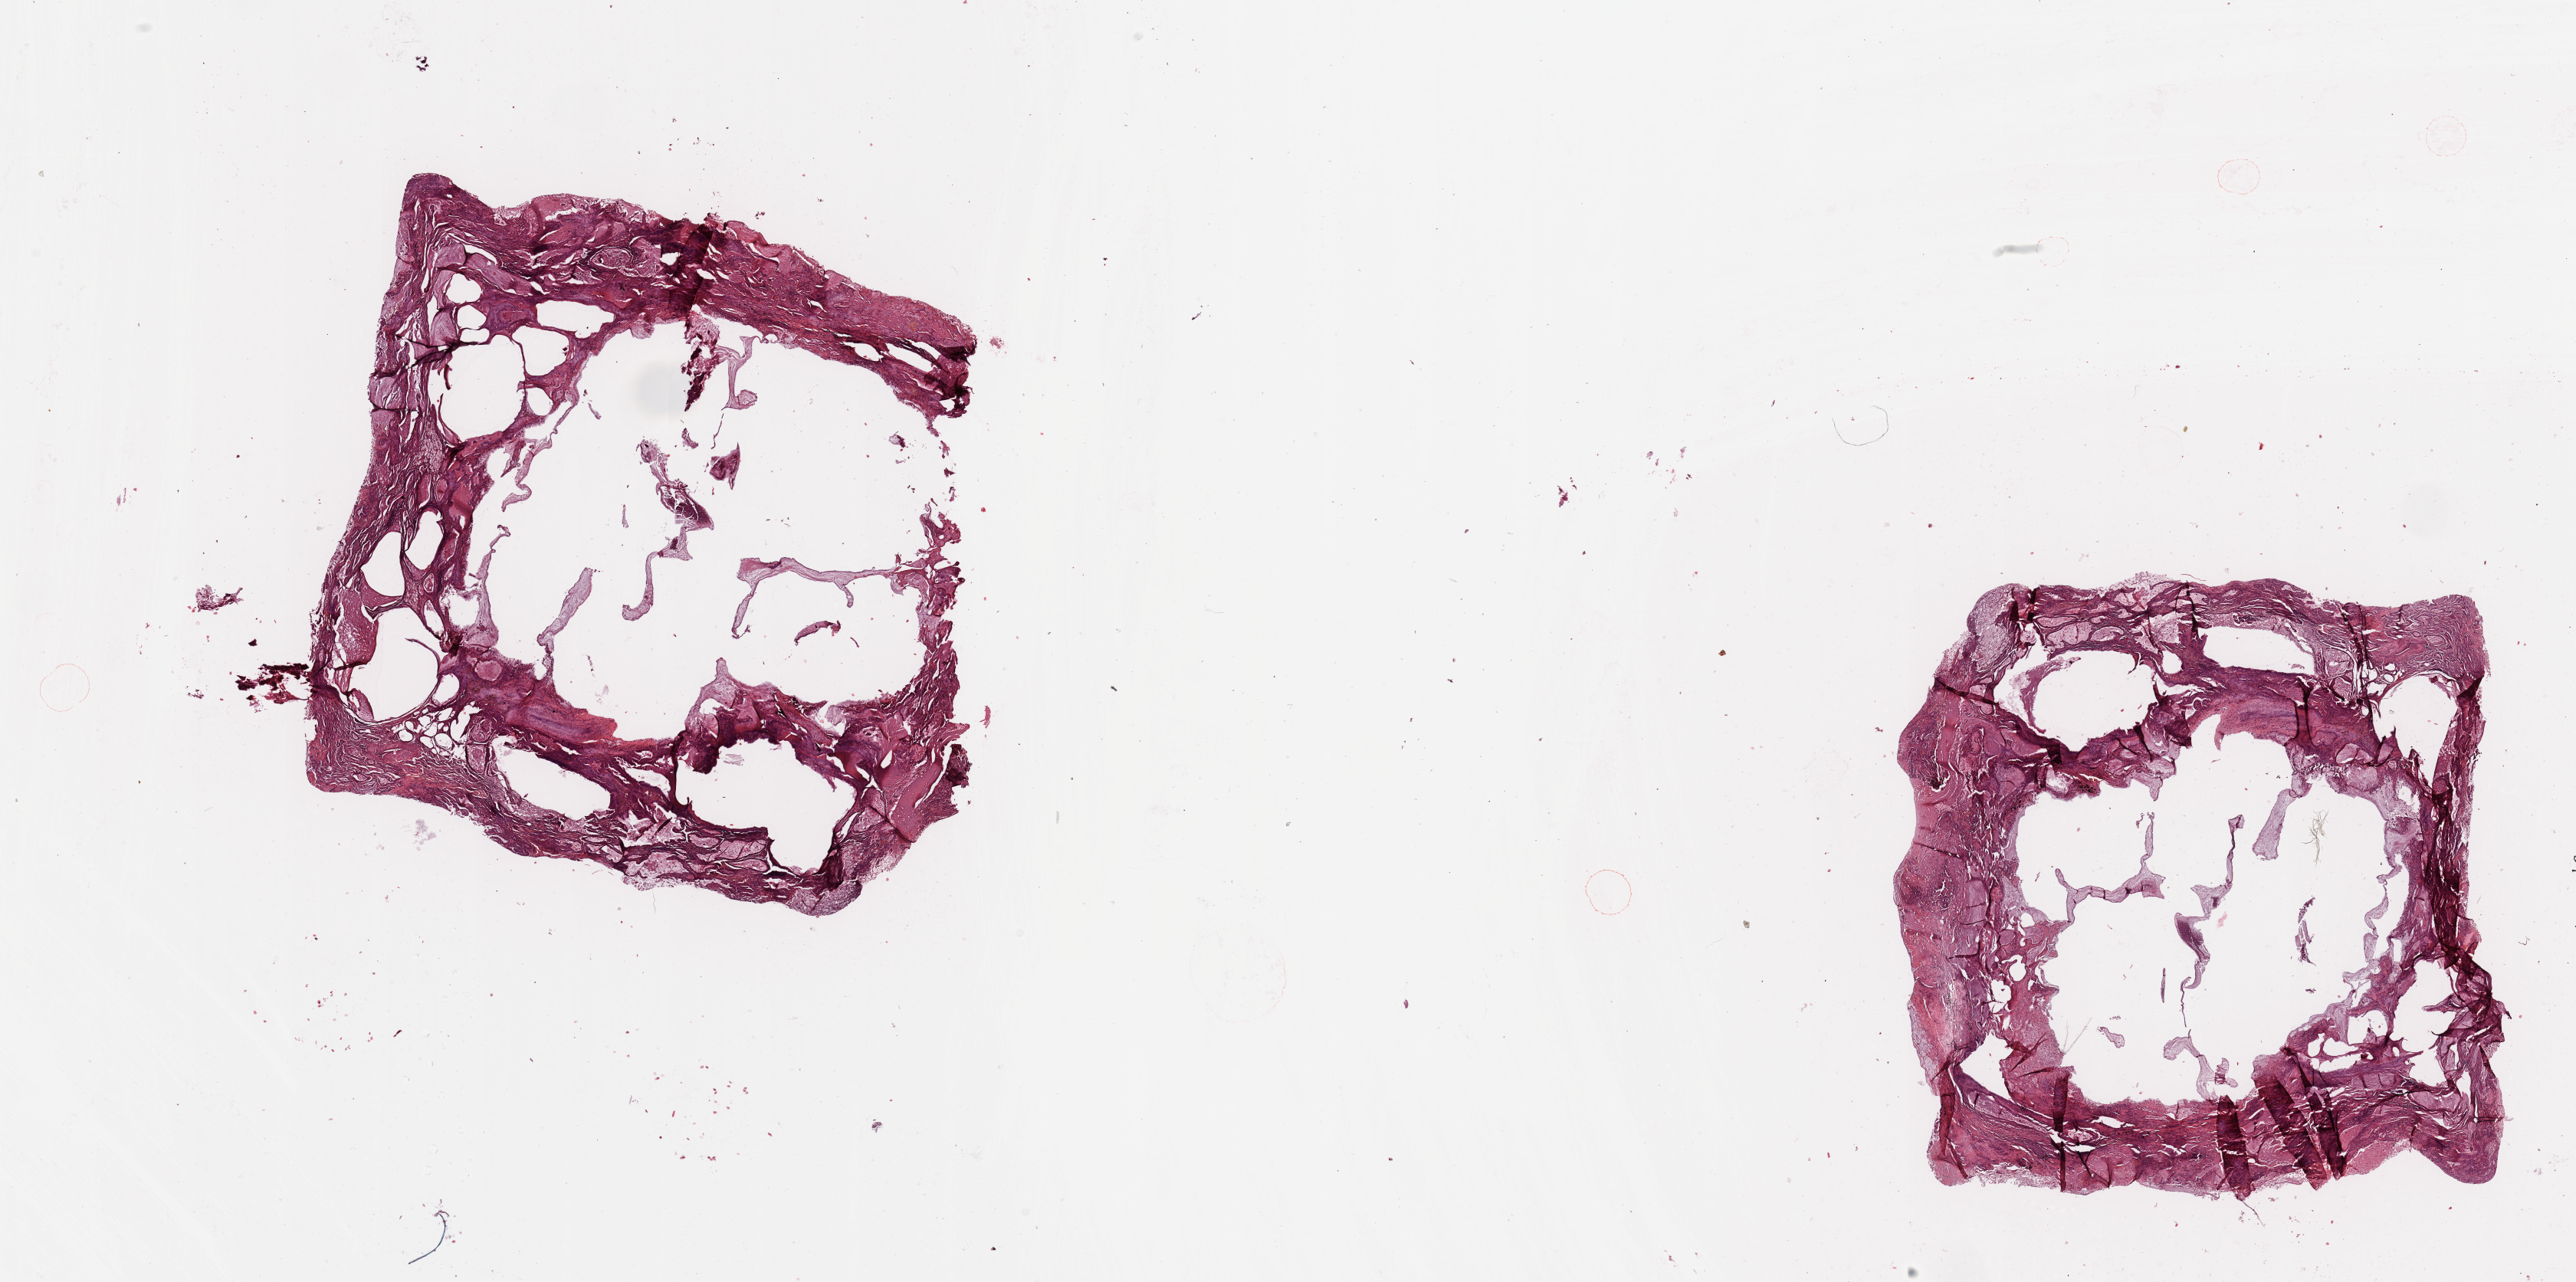
Digitized H&E-stained tissue section (whole slide) — whole scanned area (about 26.6 x 13.2 mm, acquisition: 20x scan) shown as a low-resolution overview, lung, tissue type not recorded.
Patient diagnosis (cohort enrolment): lung adenocarcinoma (lung).